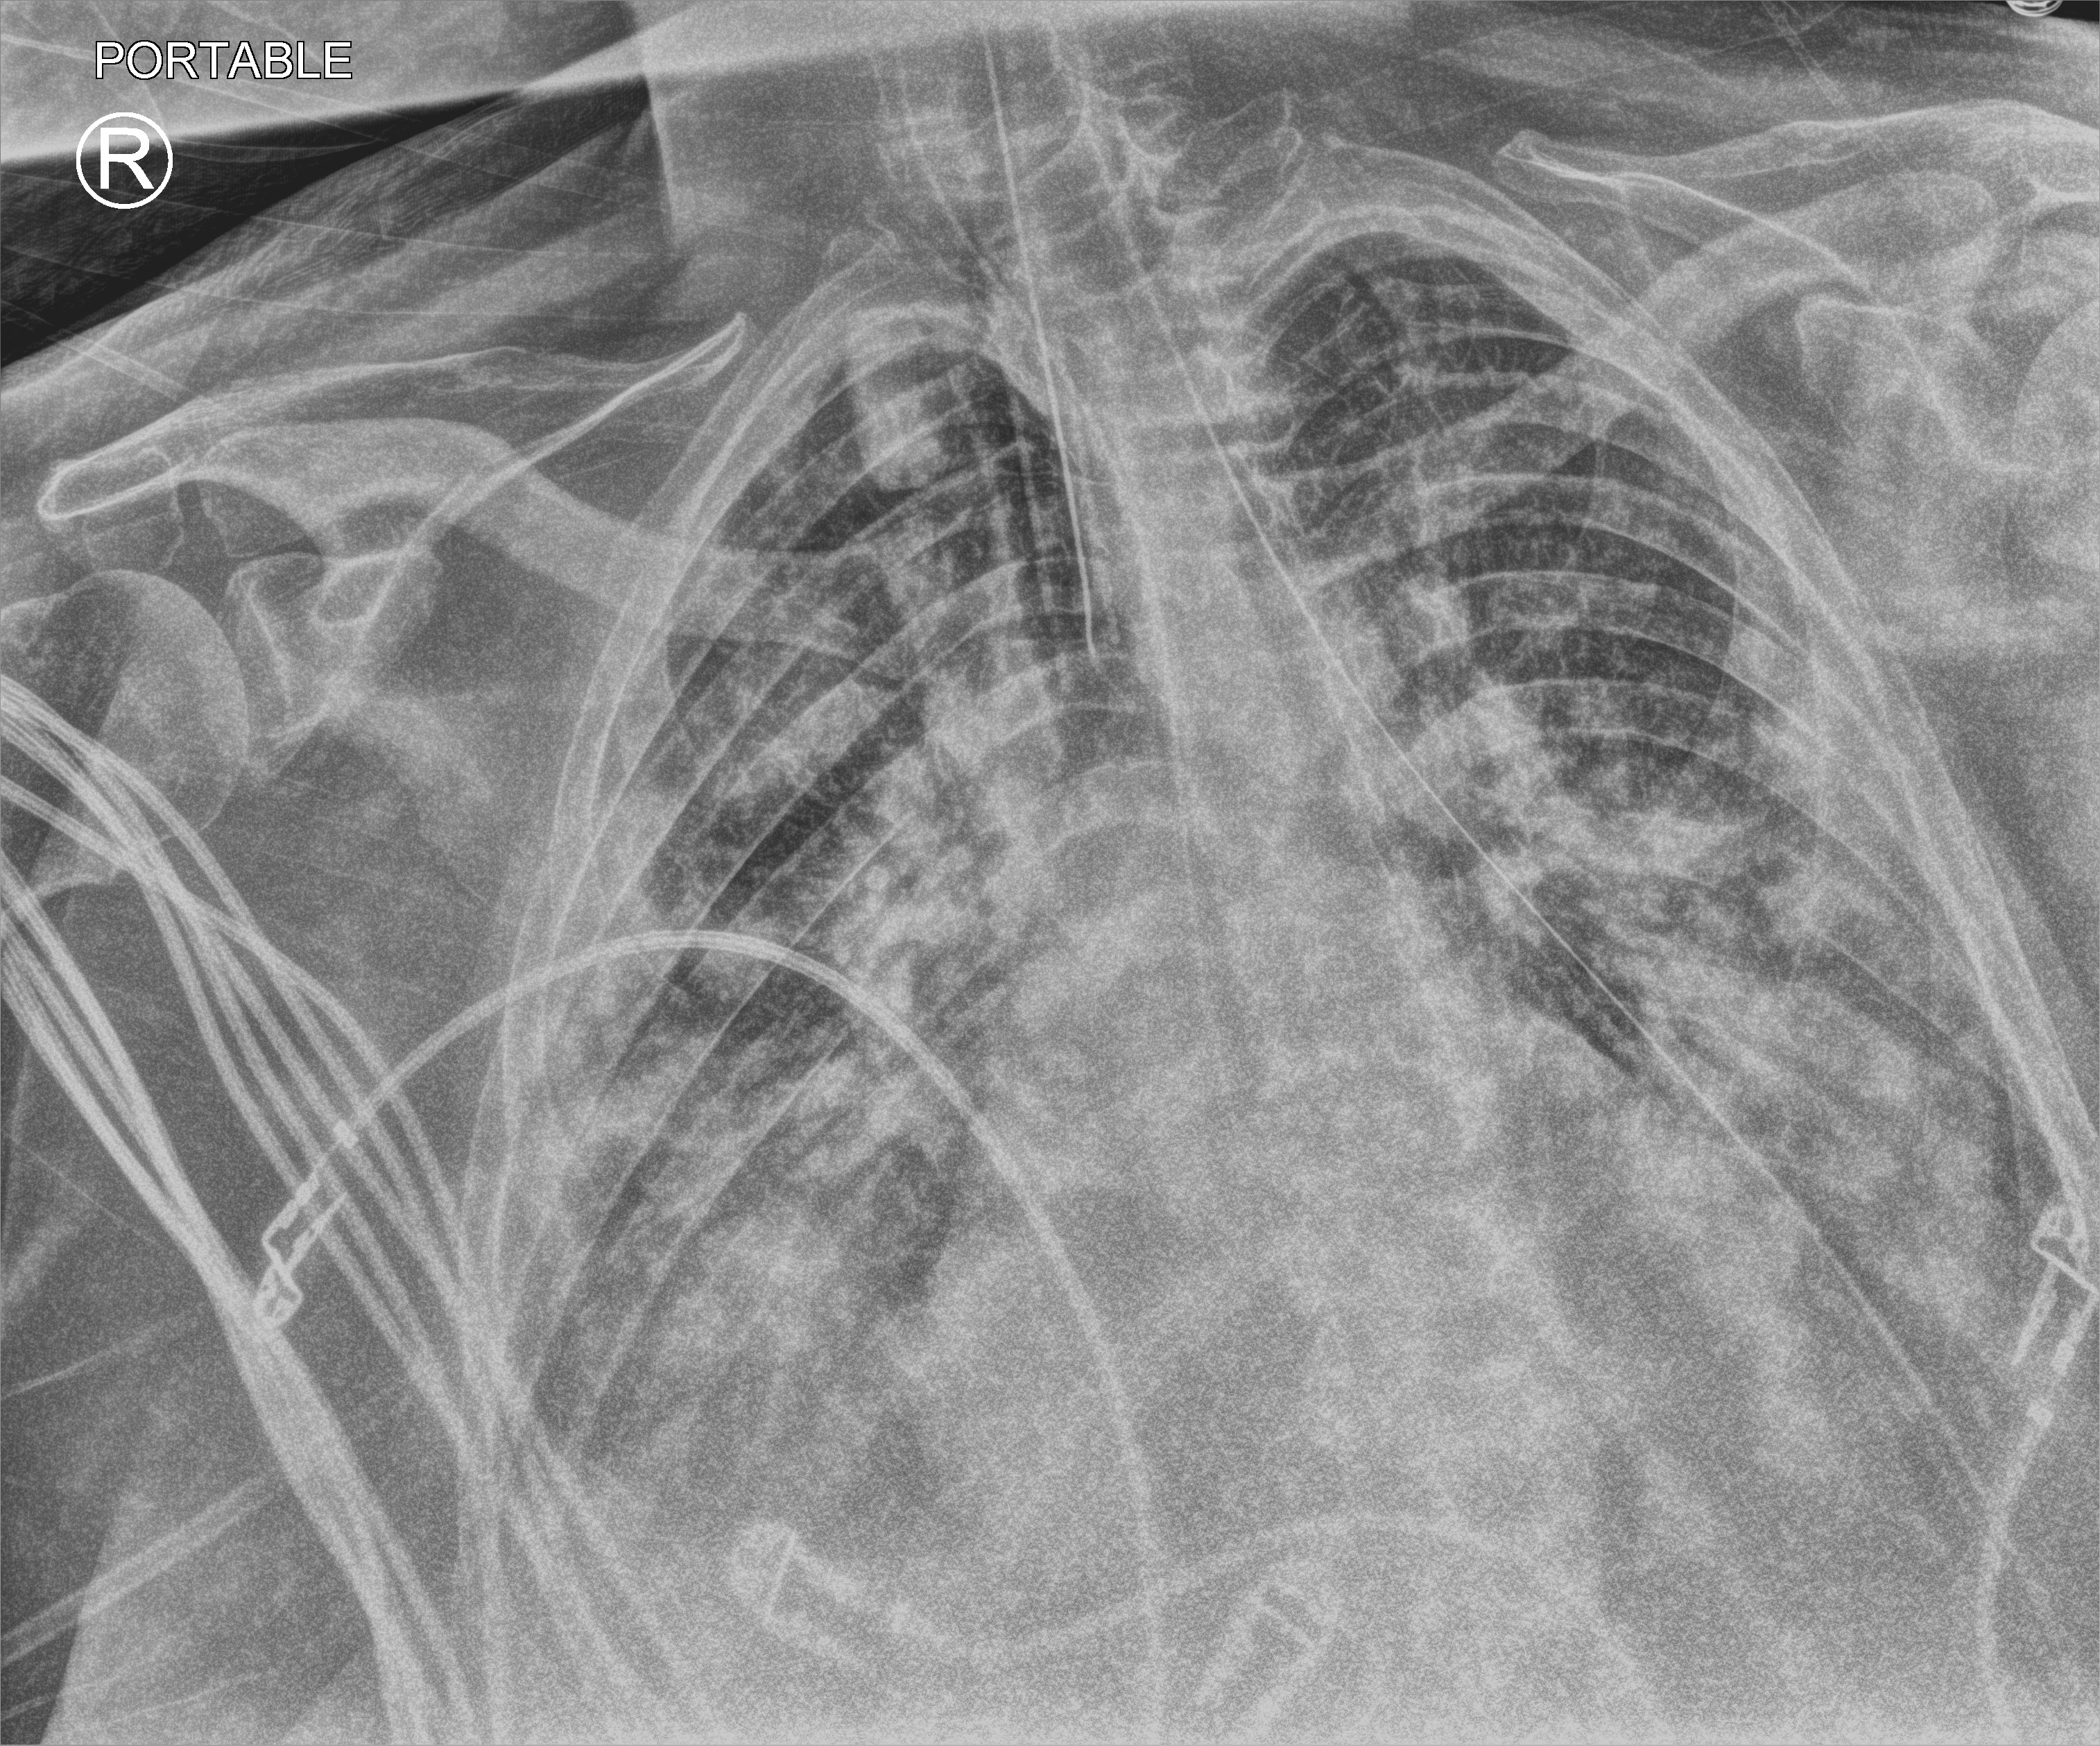
Chest X-ray (portable). Male patient hospitalised with COVID-19, age 60–74 years.
Admission-level facts for this patient (not findings on this image; timing relative to this image not recorded): mechanically ventilated during this hospital stay: yes; hypertension (admission record): yes.